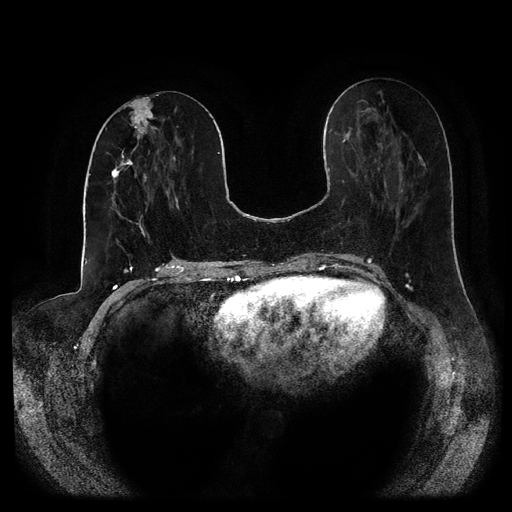
Breast MRI (dynamic contrast-enhanced, multi-phase), one axial slice. Position 41 of 116 along the scan axis. Dynamic contrast-enhanced series, time point 2 of 5 at this slice position (early post-contrast). 1.5 T. TE 2.6 ms, TR 5.2 ms. 512 × 512 image matrix. Female patient, age 53 years.
Annotated regions visible in this slice (semi-automatically segmented with operator editing):
- breast lesion (labelled 'tumour' in the annotation; benign lesions carry a separate 'benign' label): box from (x=124, y=97) to (x=155, y=140) px
- breast lesion (labelled 'tumour' in the annotation; benign lesions carry a separate 'benign' label): (x=111, y=148)–(x=133, y=180)